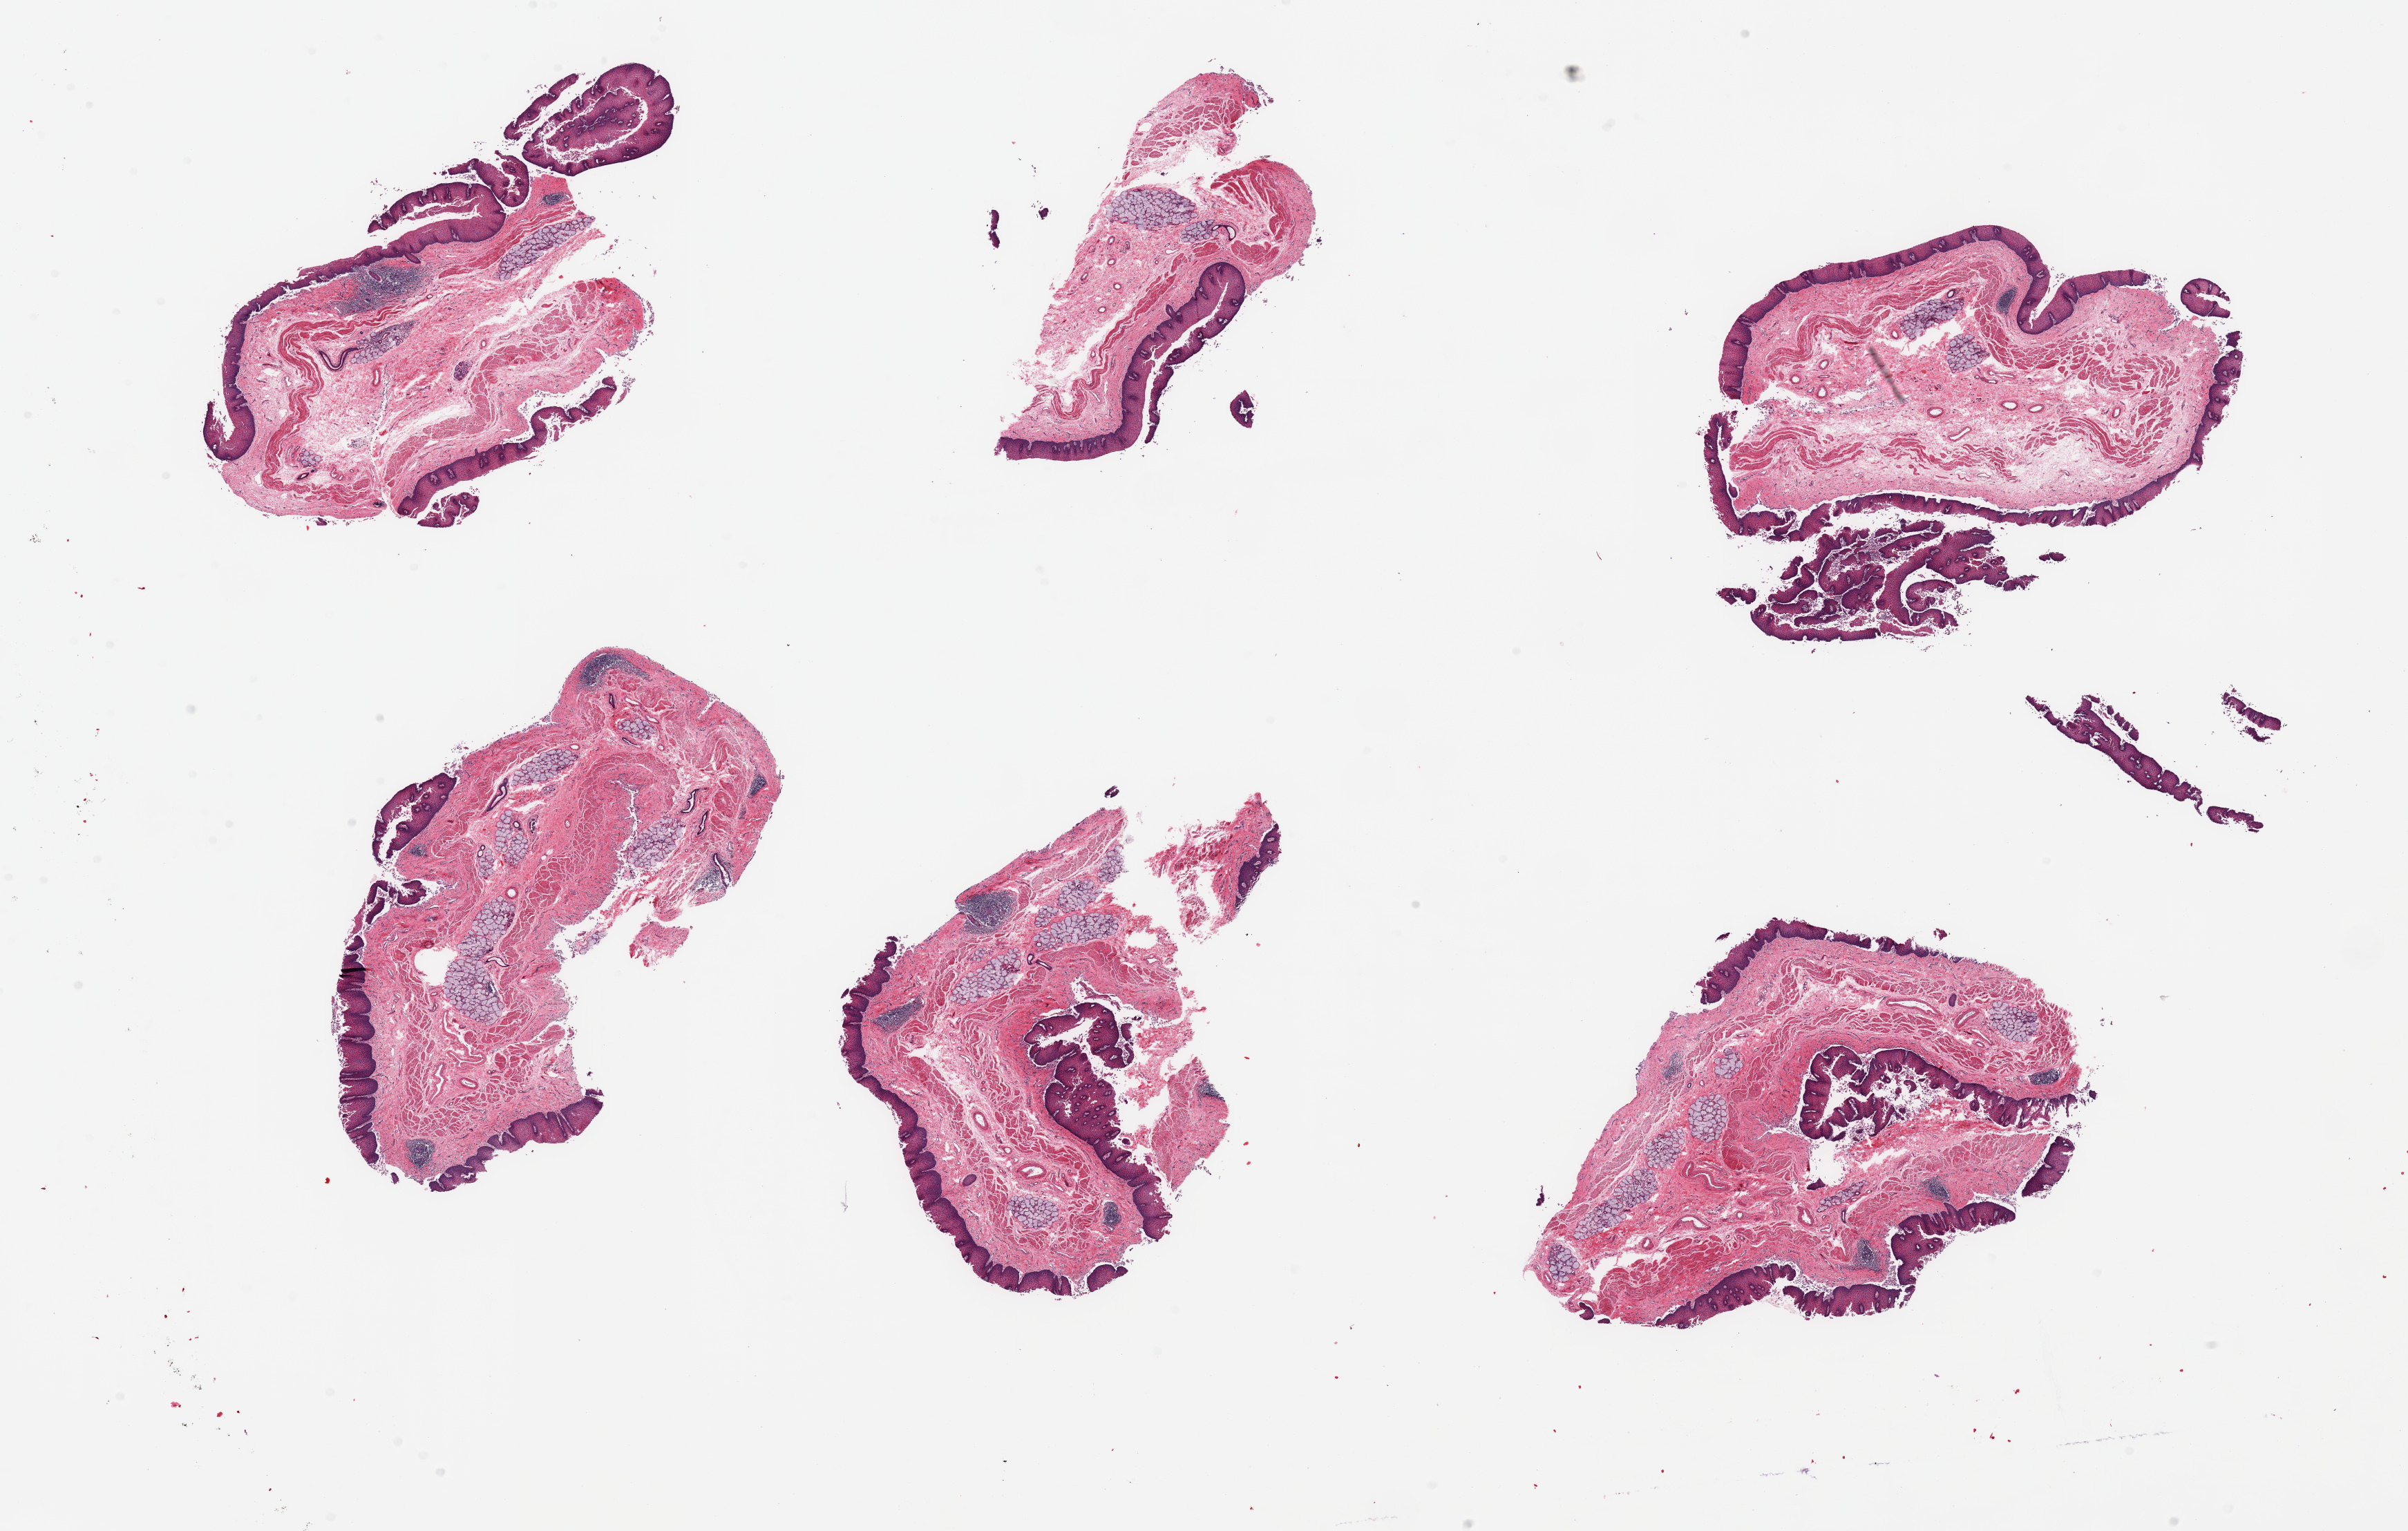
Digitized H&E-stained section, brightfield — low-resolution overview of the scanned area, about 27.6 x 17.5 mm. PAXgene-fixed, paraffin-embedded tissue. Target tissue: esophageal mucous membrane. Tissue donor sample. Male donor.
Pathologist's review note for this sample: 6 pieces, squamous mucosa beginning to slough, approaching score 2; Submucosal mucus glands present.